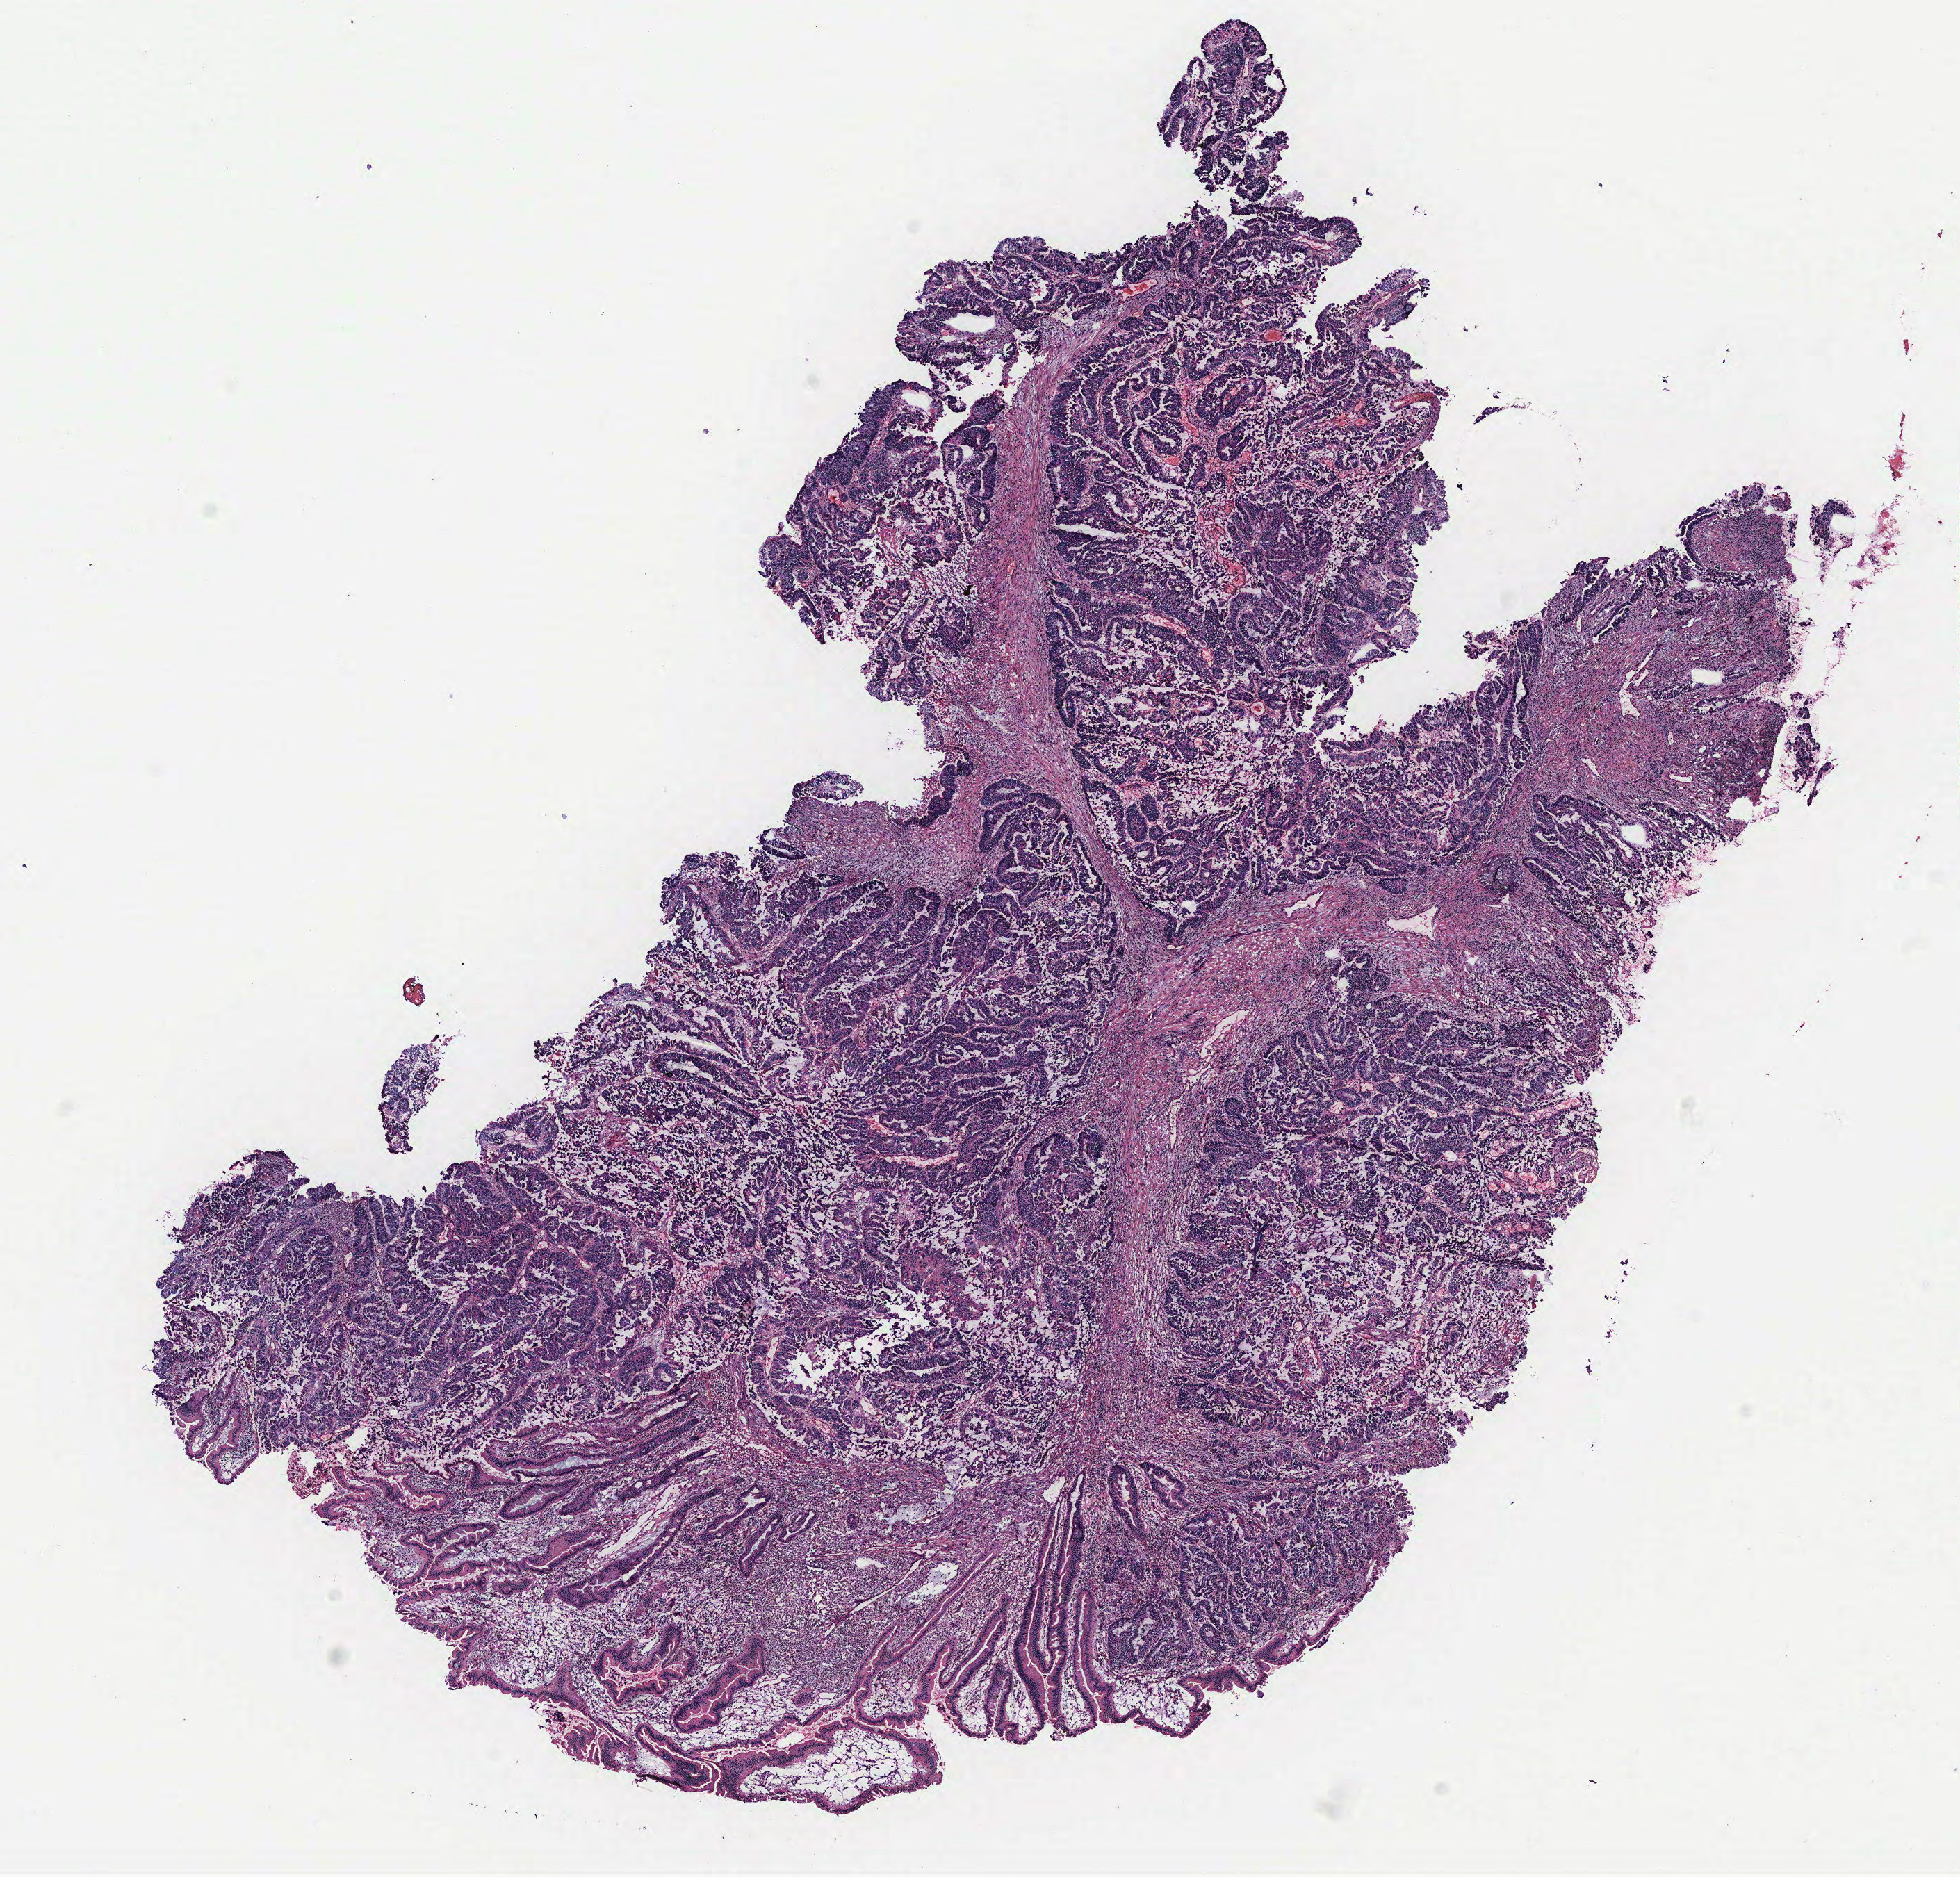
Whole-slide histology image, H&E-stained, low-resolution overview of the scanned area, about 11.3 x 10.8 mm; colon, normal (non-tumour) tissue. Patient: male, age 53 years.
This section: normal (non-tumour) tissue from the same patient. Patient diagnosis: Adenocarcinoma, NOS.